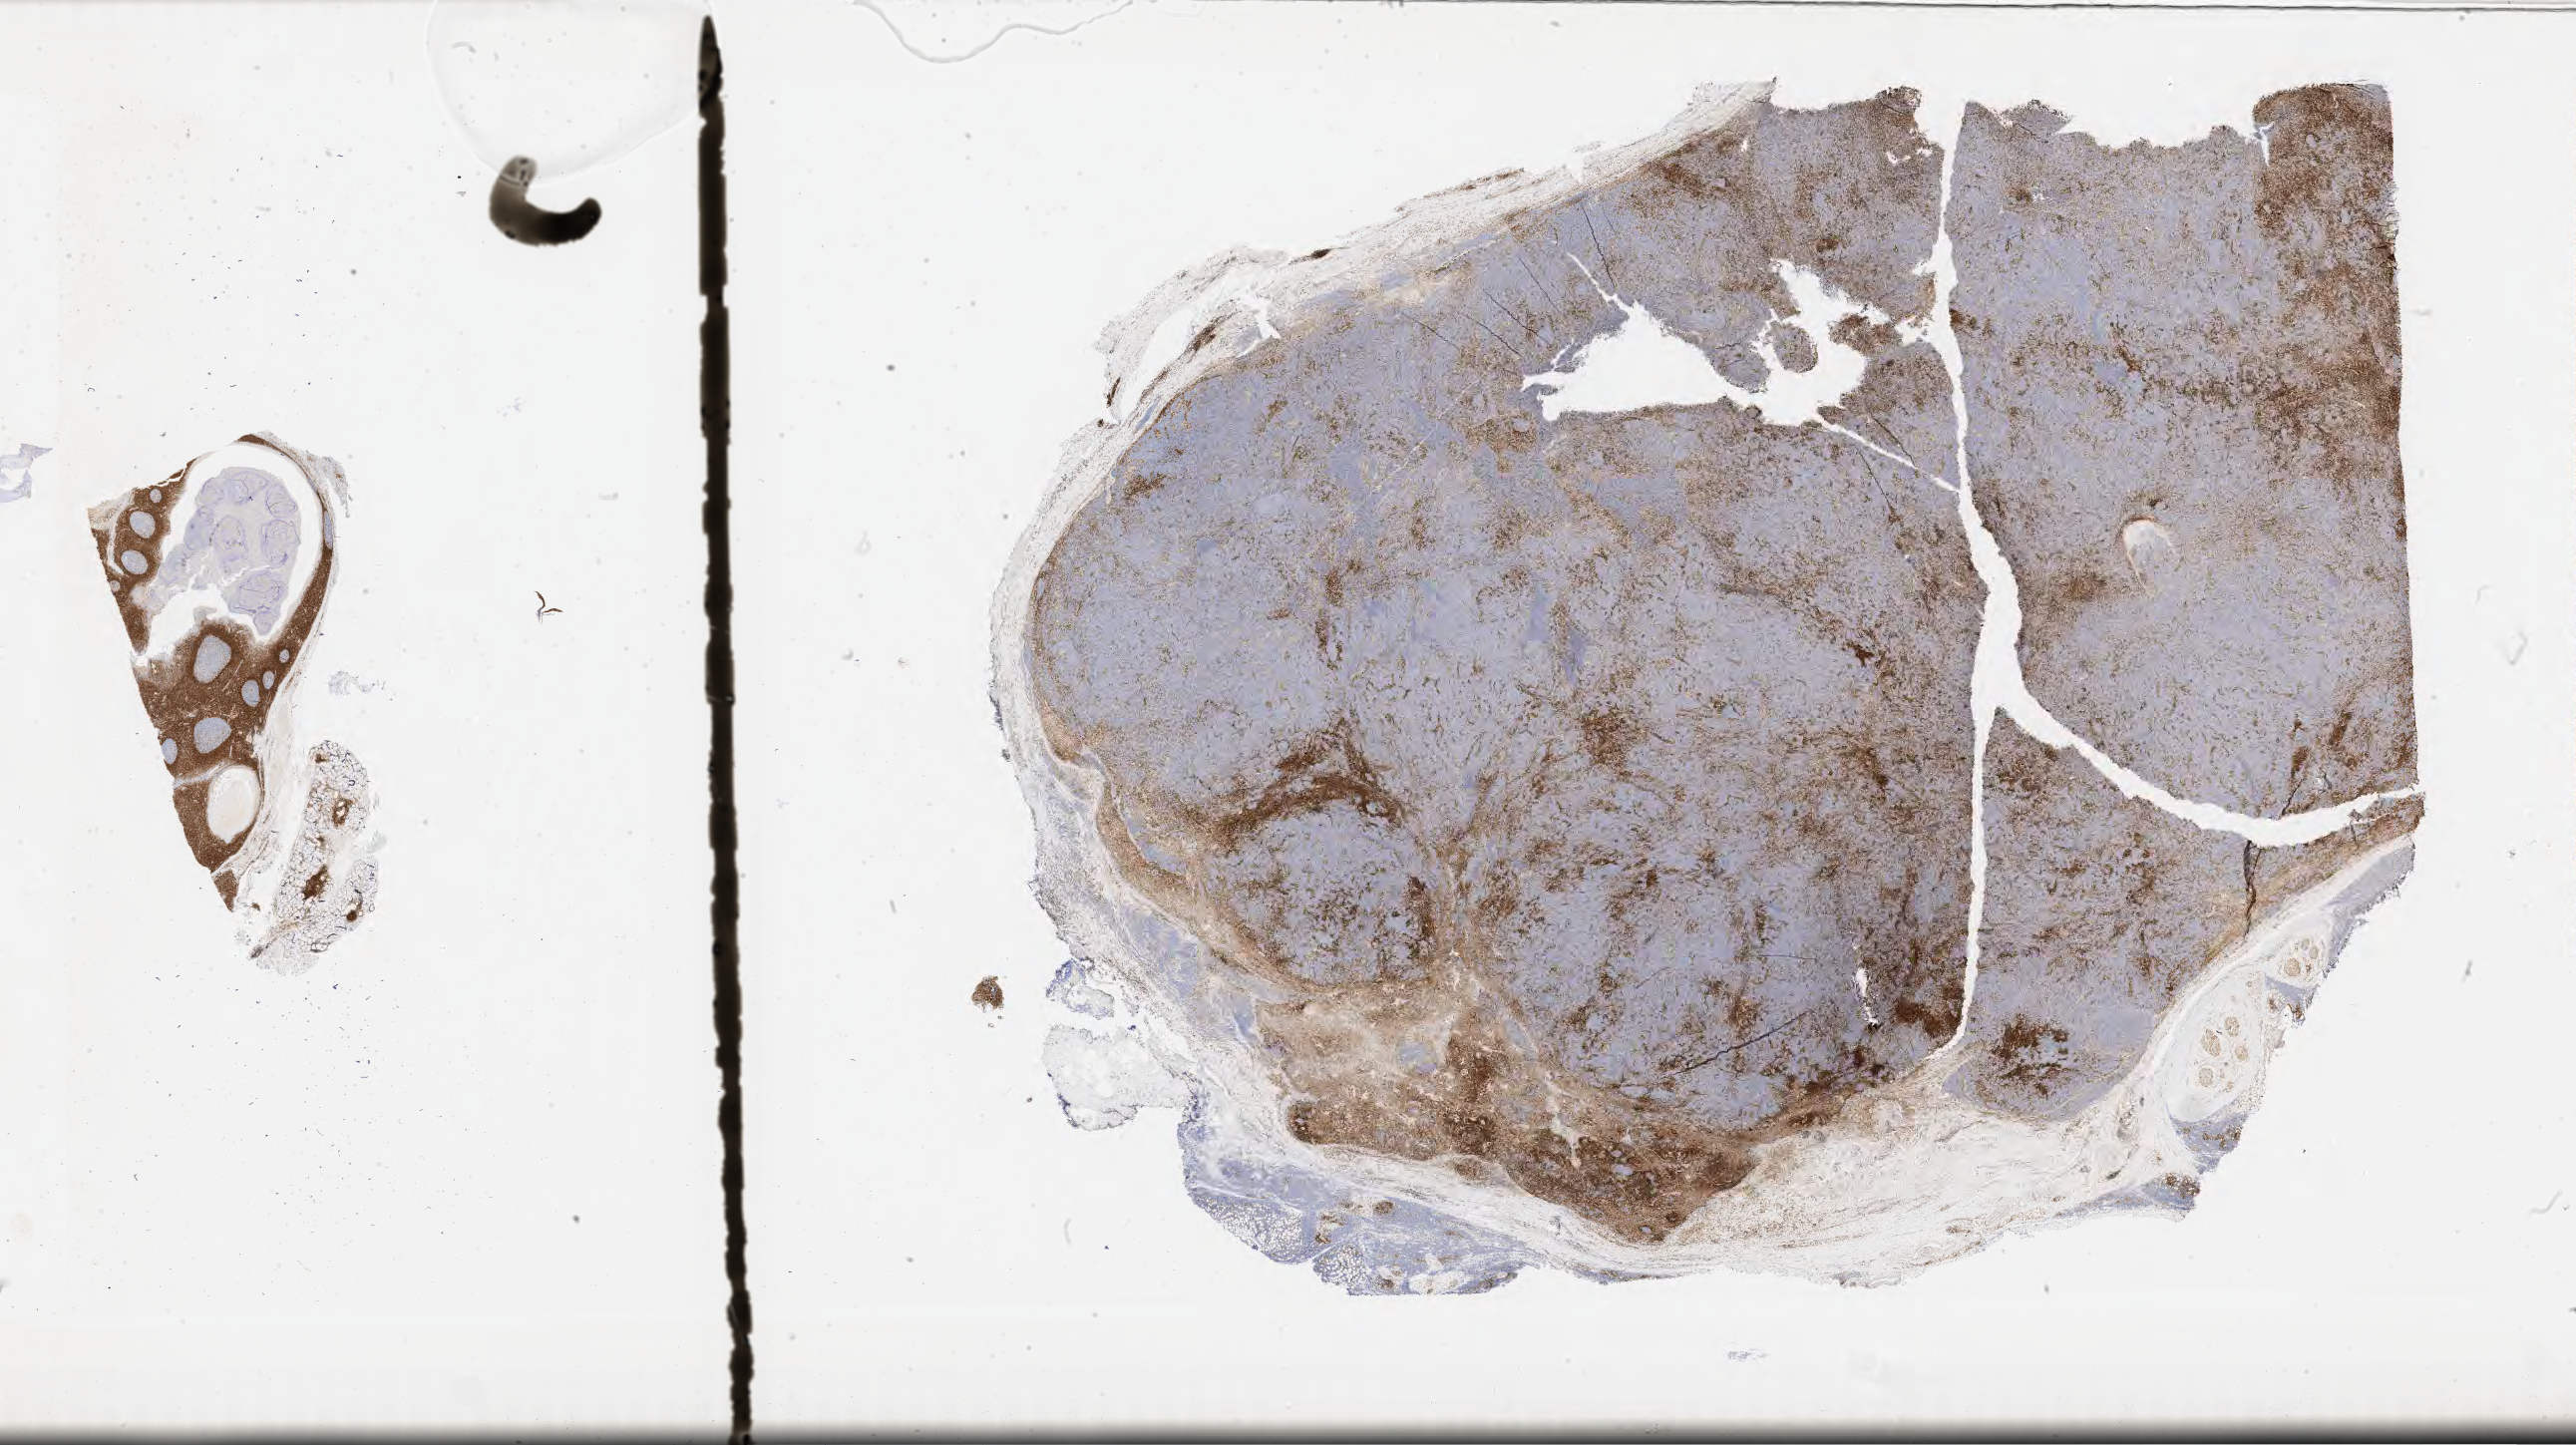
IHC for BCL2, whole-slide image — whole scanned area (about 41.8 x 23.4 mm) shown as a low-resolution overview; specimen: tumor tissue. Patient: male, aged 30.
Histologic diagnosis: Burkitt lymphoma, NOS.